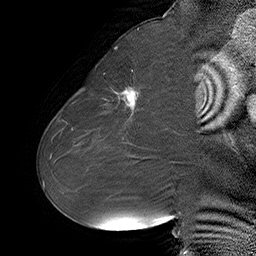
Breast MRI (dynamic contrast-enhanced), one sagittal slice; slice 28 of 55 in the series (ordered by position); dynamic contrast-enhanced series, time point 2 of 6 at this slice position (early post-contrast); 1.5 T; TE 4.5 ms, TR 32.4 ms; 256 × 256 image matrix, field of view 180 × 180 mm. Female patient. Case-level facts recorded for this patient, not image findings: setting: breast cancer imaged before/during neoadjuvant chemotherapy; receptor status: HER2-positive.
Outlined on this slice (semi-automatically segmented with operator editing):
- analysis volume of interest (the breast-tissue region the enhancement analysis was run in; not a lesion): box from (x=80, y=64) to (x=163, y=134) px
- tumour enhancement mask (voxels above the 100 % enhancement threshold inside the analysis volume of interest): (x=114, y=87)–(x=138, y=111)